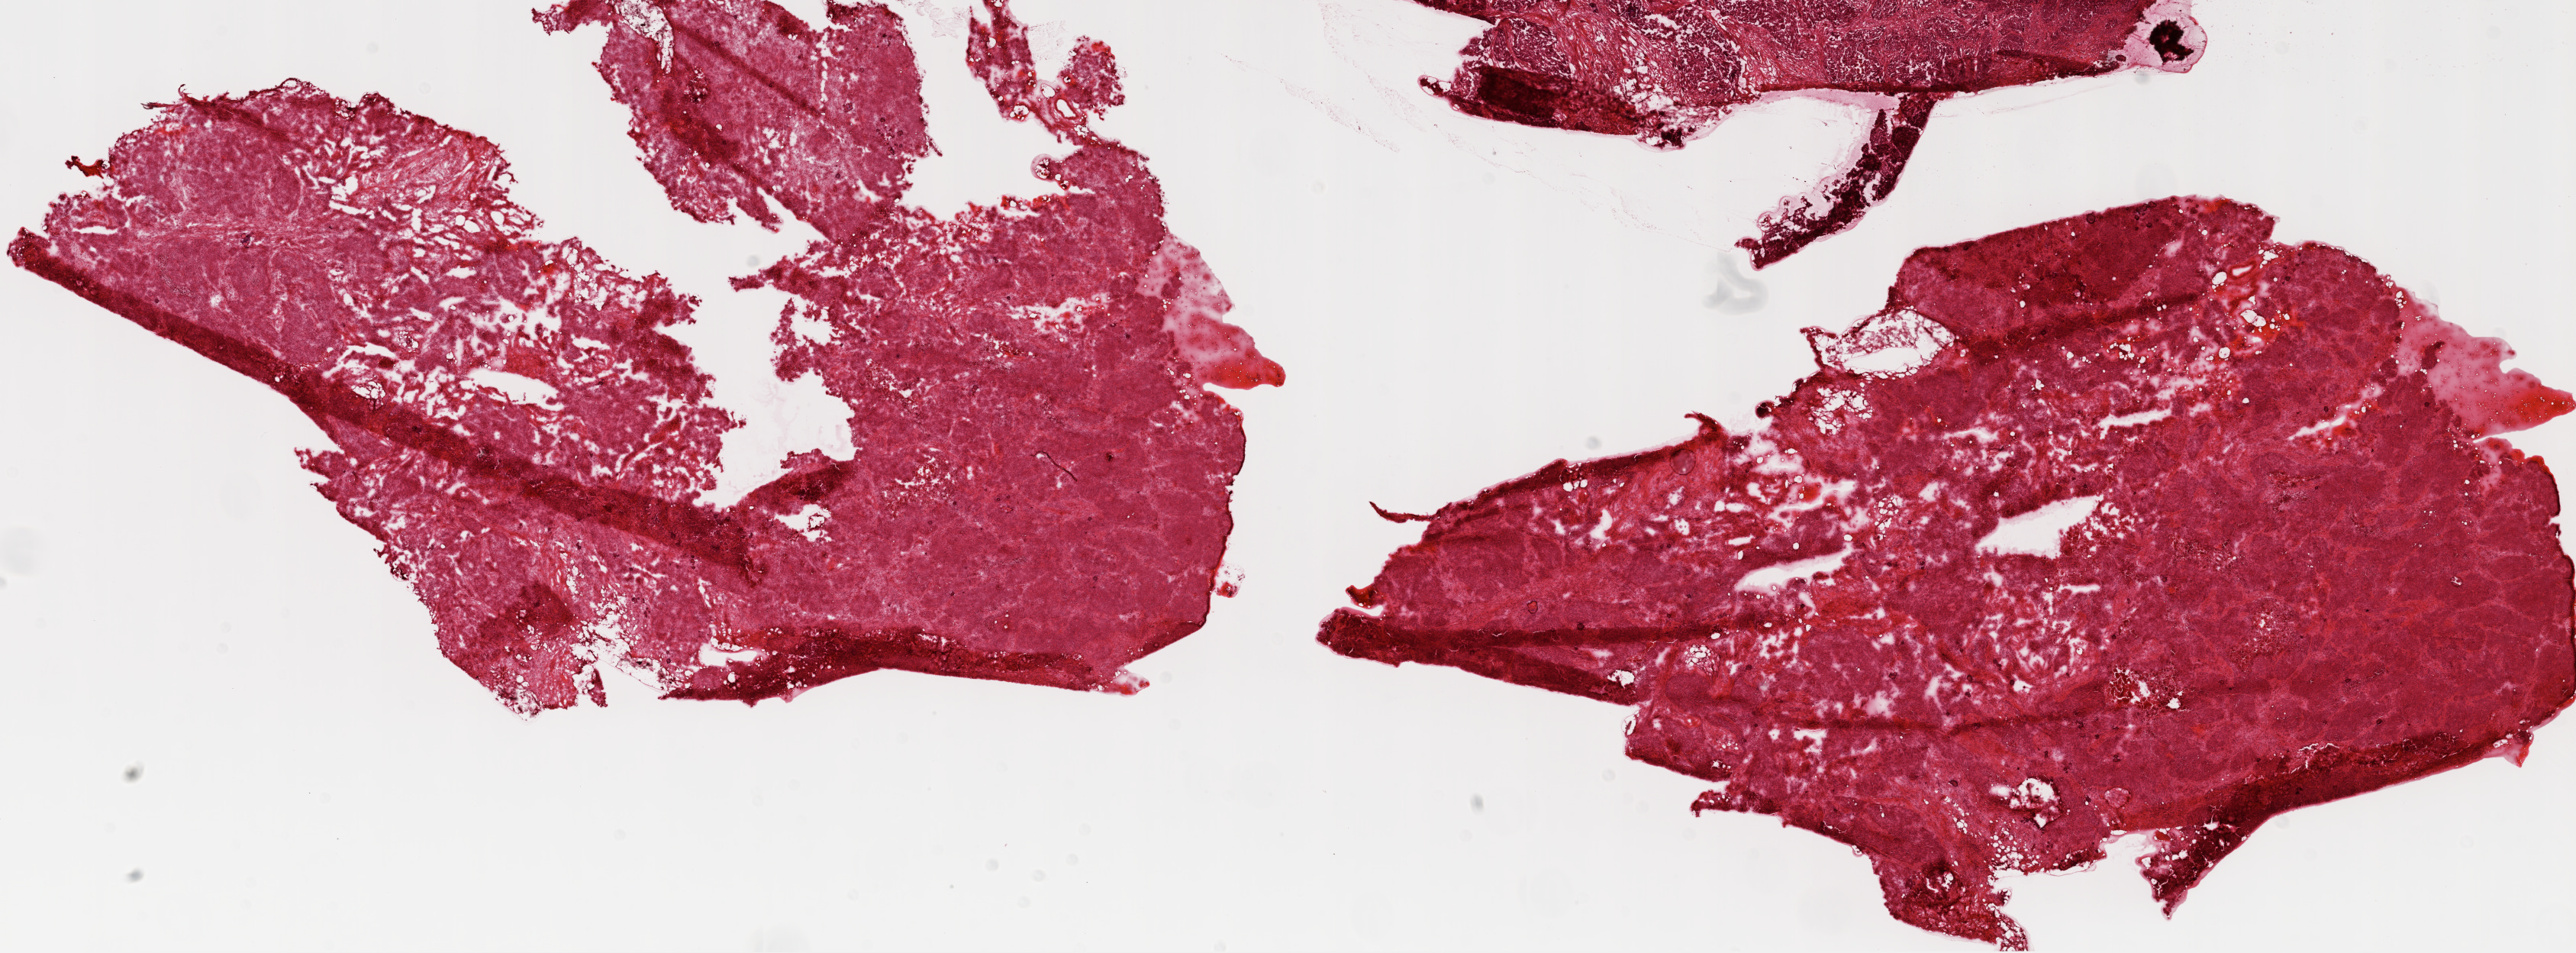
Whole-slide histology image, H&E — low-resolution overview of the scanned area, about 27.1 x 10.0 mm (slide scanned at 20x), frozen section from the top of the tissue portion, ovary, primary tumour sample. Patient: female, age at initial diagnosis 67 years. Histologic grade: G3 (poorly differentiated). Pathologist review of this section (percent, as recorded): tumour cells 80%, tumour nuclei 90%, normal cells 0%, stromal cells 10%, necrosis 10%.
- FIGO stage: IIIC
- pathologic diagnosis: Serous cystadenocarcinoma, NOS
- laterality: bilateral